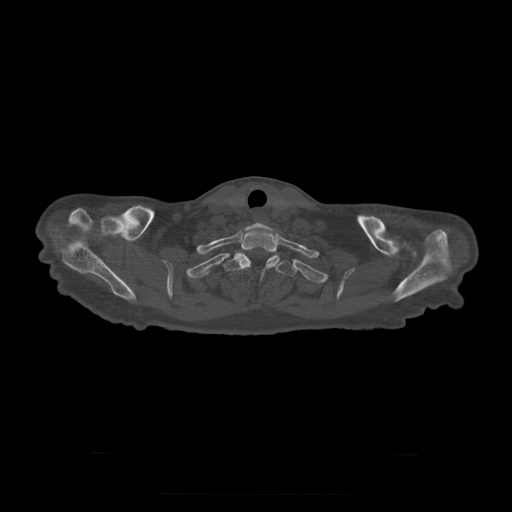
CT including the spine, one axial slice. Slice 282 of 397 in the series (ordered by position). Reconstruction kernel STANDARD. Bone window (W 1800 / L 400 HU). 1.25 mm slice thickness. 512 × 512 image matrix, field of view 510 × 510 mm. Patient age 73 years. Case-level facts recorded for this patient, not image findings: primary cancer: prostate.
Structures marked on this image (semi-automatic segmentation, software-assisted and operator-edited):
- T1 vertebra: box from (x=238, y=231) to (x=280, y=268) px
- T2 vertebra: (x=223, y=254)–(x=297, y=277)